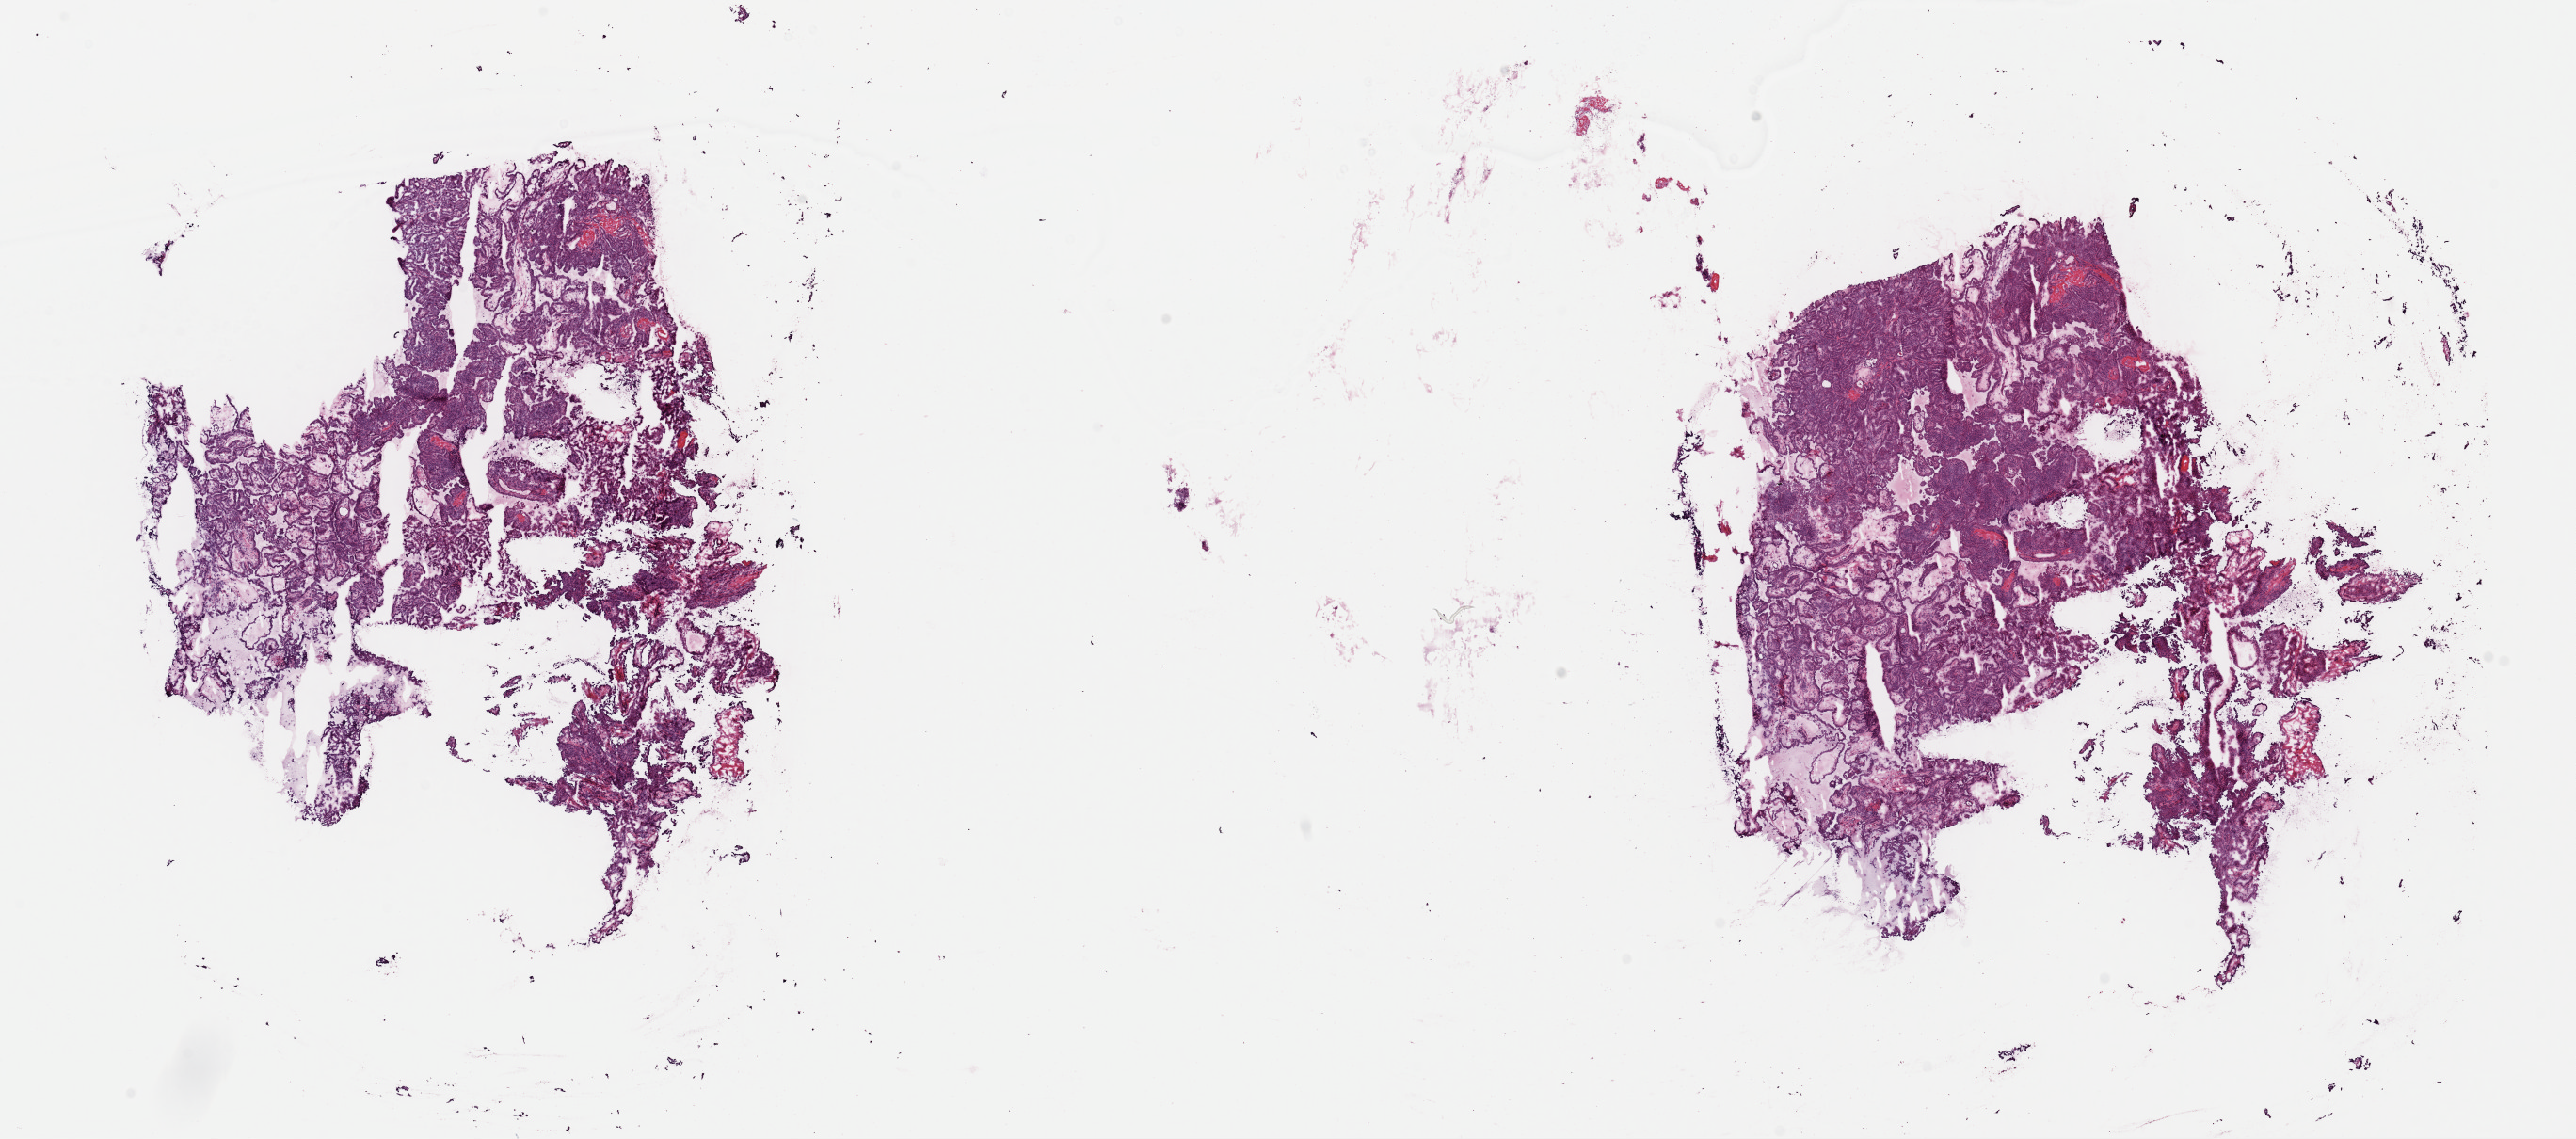
Digitized H&E-stained tissue section (whole slide), shown as a low-resolution overview of the whole scanned area (about 21.6 x 9.6 mm, acquisition: 40x scan), frozen section from the top of the tissue portion, thyroid, primary tumour sample. Female patient; age at initial diagnosis 30 years. Pathologist review of this section (percent, as recorded): tumour cells 100%, tumour nuclei 95%, normal cells 0%, stromal cells 0%, necrosis 0%. Inflammatory infiltration, as recorded: lymphocyte infiltration 0%, monocyte infiltration 0%, neutrophil infiltration 0%.
Histologic diagnosis: Papillary adenocarcinoma, NOS (thyroid gland). Lymph nodes positive (case pathology): 3 of 3 examined. AJCC pathologic stage: I (6th edition).